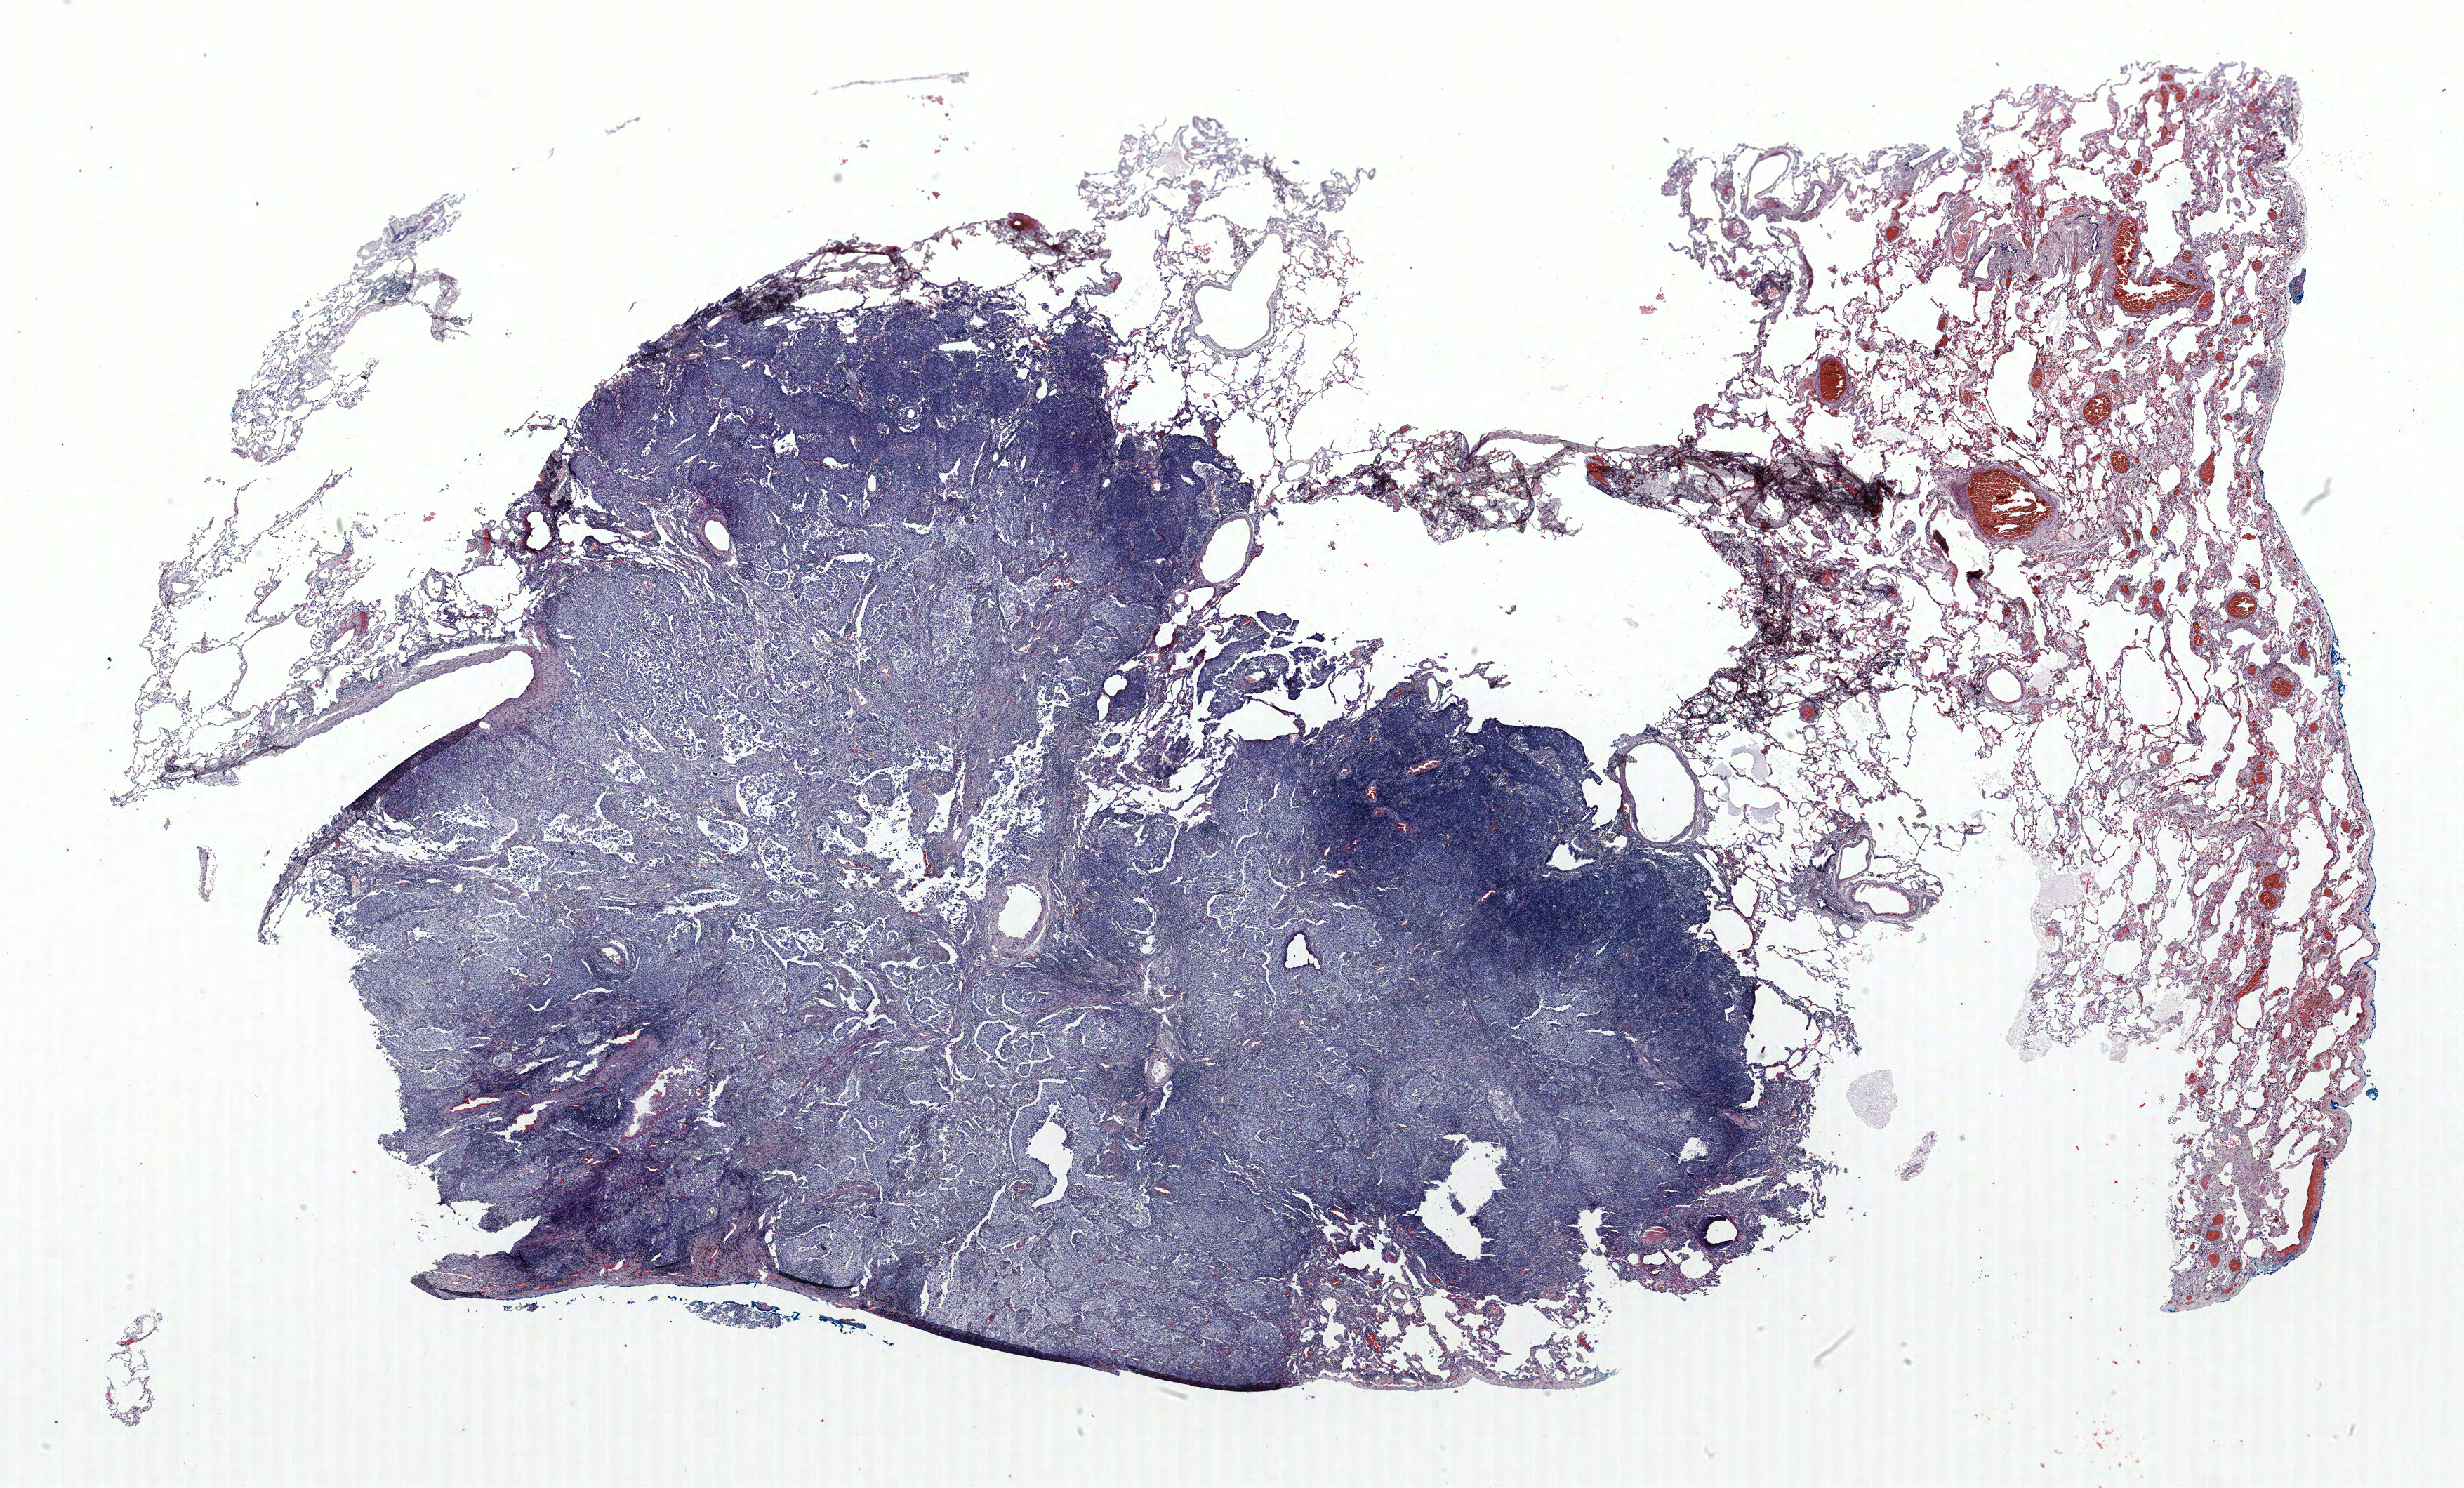
H&E whole-slide image — whole scanned area (about 28.1 x 17.0 mm, acquisition: 40x scan) shown as a low-resolution overview. FFPE section. Lung tissue. Male, age 72 at enrolment. Grade: moderately differentiated (G2).
Tumour size (pathology): 25 mm. Primary tumour location (clinical record): right upper lobe. Participant's lung-cancer diagnosis: Squamous cell carcinoma, NOS. Stage (AJCC 6th edition): IIA.